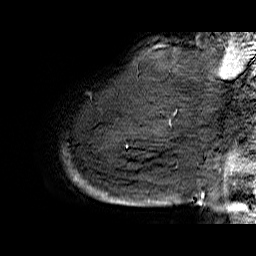
Breast MRI (dynamic contrast-enhanced), one sagittal slice; slice 53 of 60 in the series (ordered by position); dynamic contrast-enhanced series, time point 2 of 6 at this slice position (early post-contrast); 1.5 T; TE 6.4 ms, TR 32.9 ms; 4 mm slice thickness; 256 × 256 image matrix. Female patient. Case-level facts recorded for this patient, not image findings: setting: breast cancer imaged before/during neoadjuvant chemotherapy; receptor status: HR-positive, HER2-negative.
Annotated regions visible in this slice (semi-automatic segmentation, software-assisted and operator-edited):
- analysis volume of interest (the breast-tissue region the enhancement analysis was run in; not a lesion): bounding box <65,74,176,207> (left, top, right, bottom; pixels)
- tumour enhancement mask (voxels above the 100 % enhancement threshold inside the analysis volume of interest): <73,112,176,181>